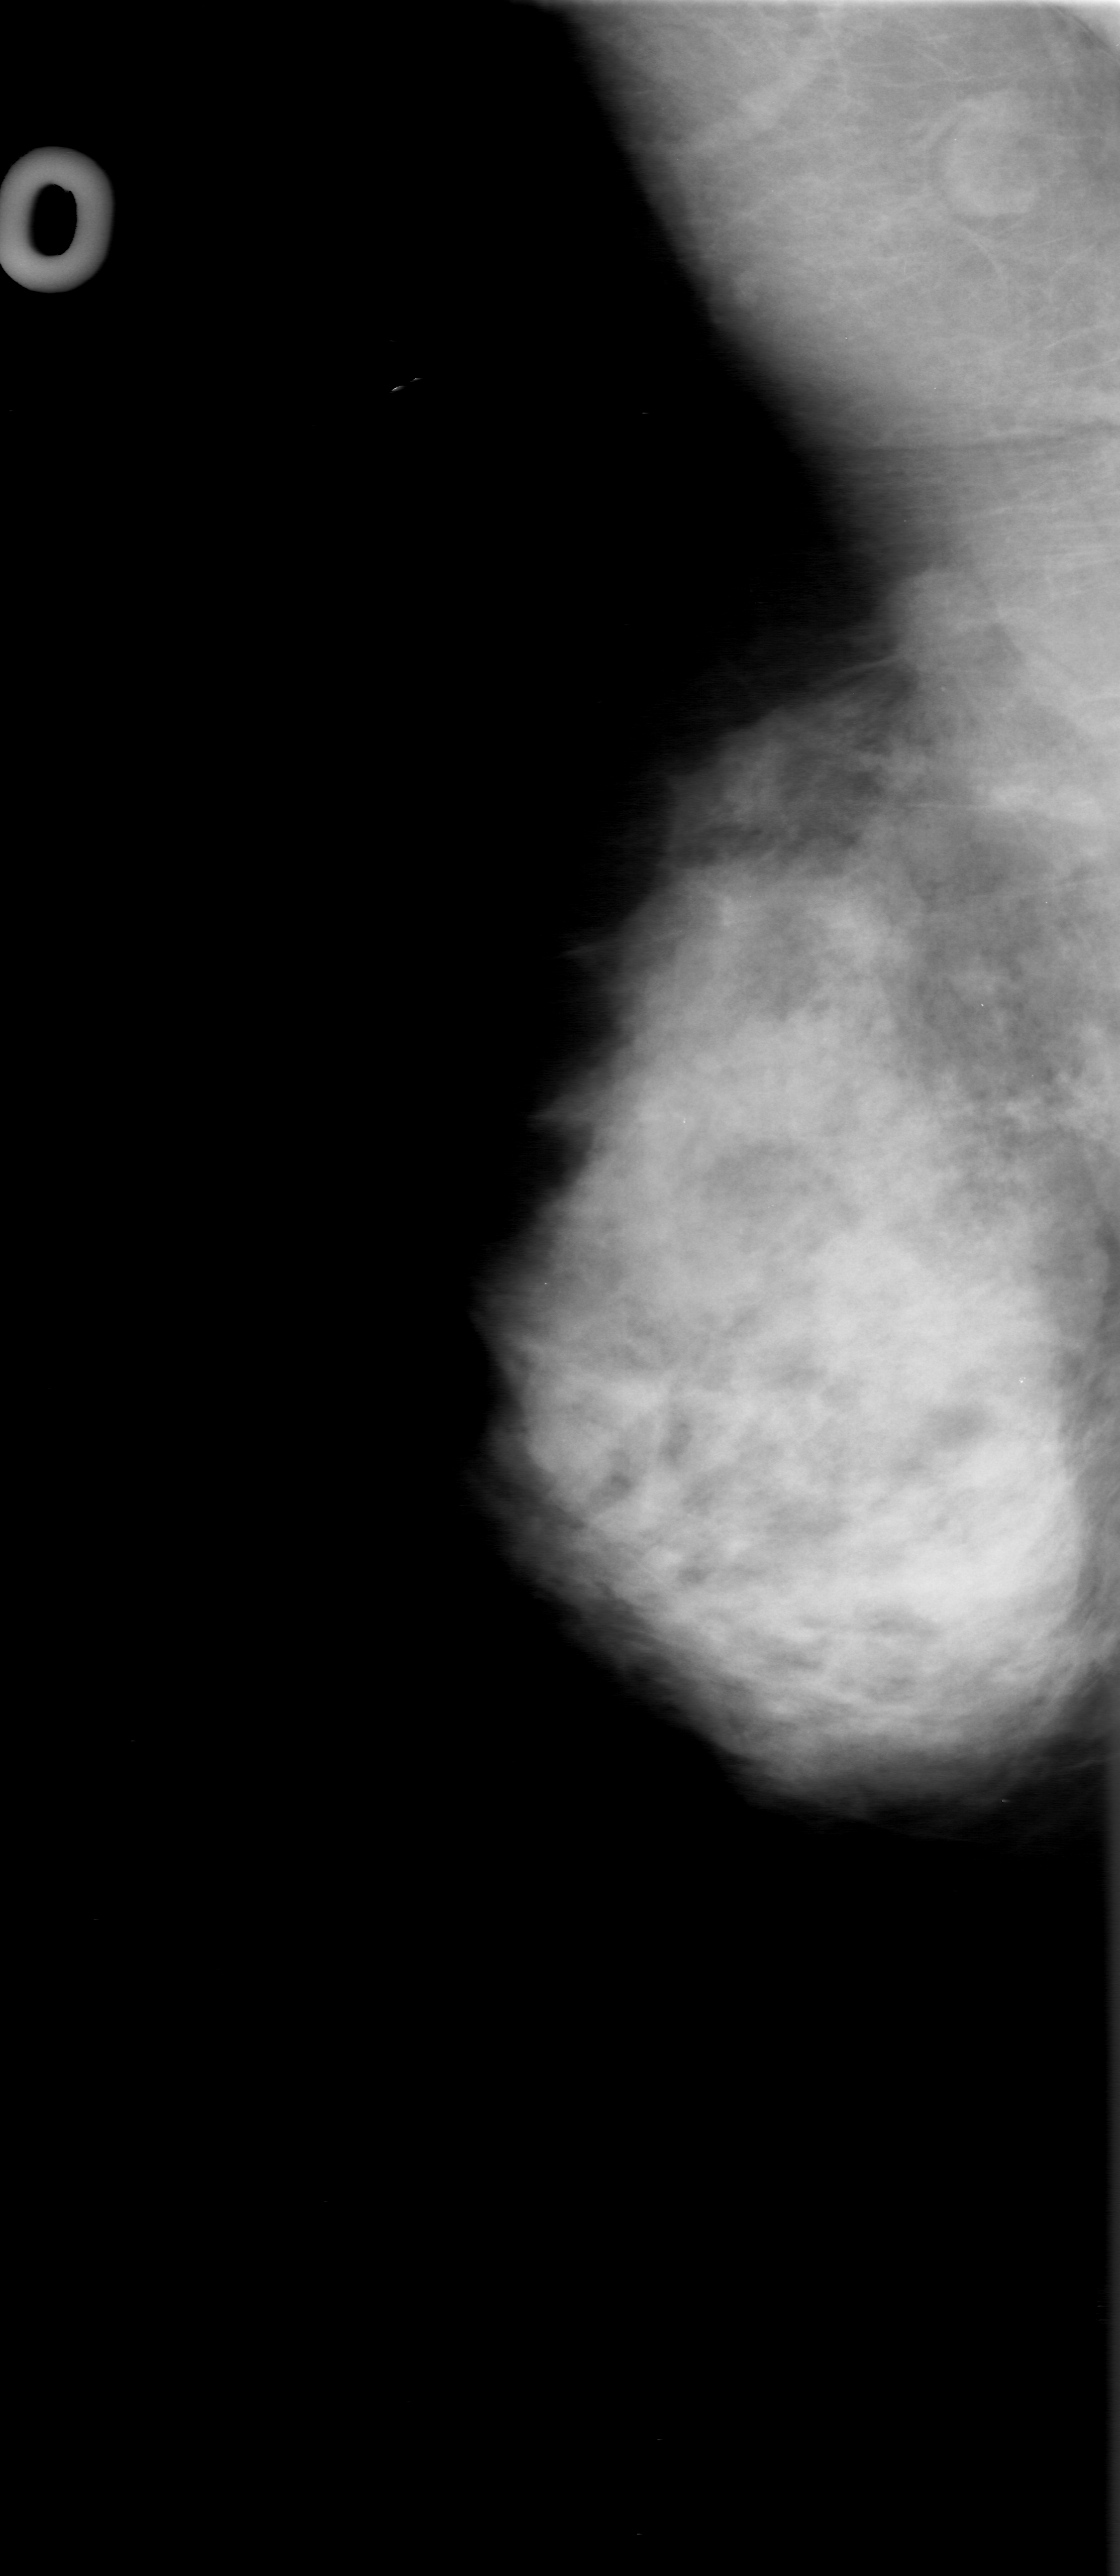
Digitized screen-film mammogram, right breast, MLO view.
Marked abnormality: mass, shape round, margins spiculated; BI-RADS assessment category 3; pathology (as recorded): malignant.